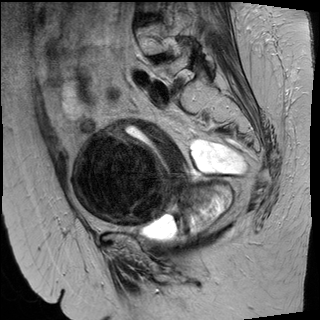
Pelvic MRI for cervical cancer, one sagittal slice. Slice 21 of 50 in the series (ordered by position). T2-weighted. 1.5 T. TE 89 ms, TR 4880 ms. 320 × 320 image matrix, field of view 260 × 260 mm. Female patient, age 50 years.
Annotated regions visible in this slice (expert manual segmentation):
- uterus and cervix: bounding box [x1, y1, x2, y2] px = [73, 117, 231, 230]